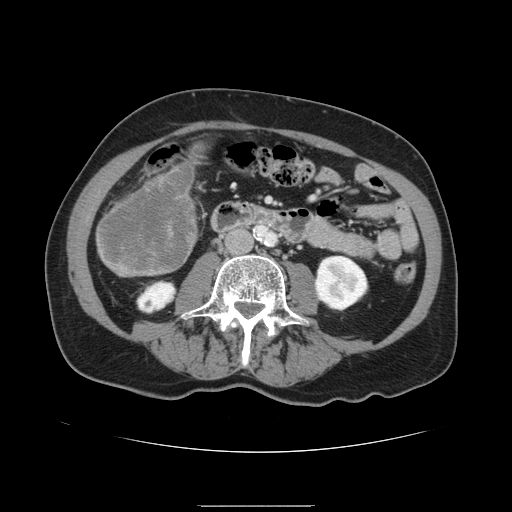
Contrast-enhanced abdominal CT, one axial slice. Position 29 of 168 along the scan axis. Intravenous contrast given. Soft-tissue window (W 400 / L 40 HU). 2.5 mm slice thickness. 512 × 512 image matrix, field of view 386 × 386 mm. Male patient, age 74 years. From the clinical record (not read from this slice): diagnosis: colorectal cancer liver metastases, imaged before liver resection; multiple liver metastases: no; largest metastasis: 14.5 cm; chemotherapy before resection: no.
Annotated regions visible in this slice (manually delineated by an expert):
- liver: box from (x=95, y=153) to (x=200, y=277) px
- liver metastasis: (x=99, y=165)–(x=194, y=272)